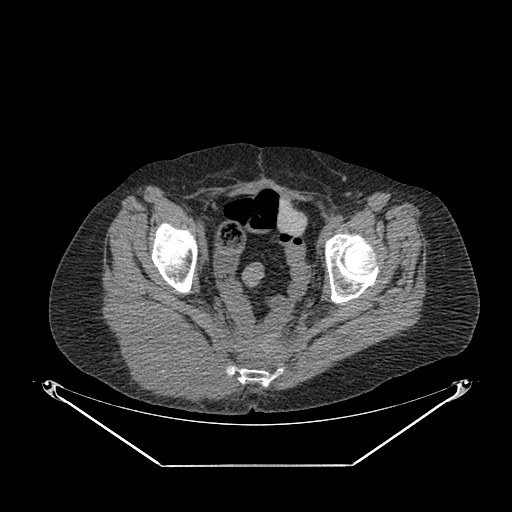
CT of an extremity soft-tissue mass (from a PET/CT study), one axial slice. Position 60 of 267 along the scan axis. Reconstruction kernel SOFT. 140 kVp. Soft-tissue window (W 400 / L 40 HU). 512 × 512 image matrix, field of view 500 × 500 mm. Female patient. Case-level facts recorded for this patient, not image findings: histological type: spindle cell suggestive of myxofibrosarcoma; grade: intermediate; site of the primary tumour: right buttock.
Annotated regions visible in this slice (expert contour drawn on MRI and transferred to this co-registered scan by the dataset authors):
- gross tumour volume (mass): bounding box <114,315,231,401> (left, top, right, bottom; pixels)